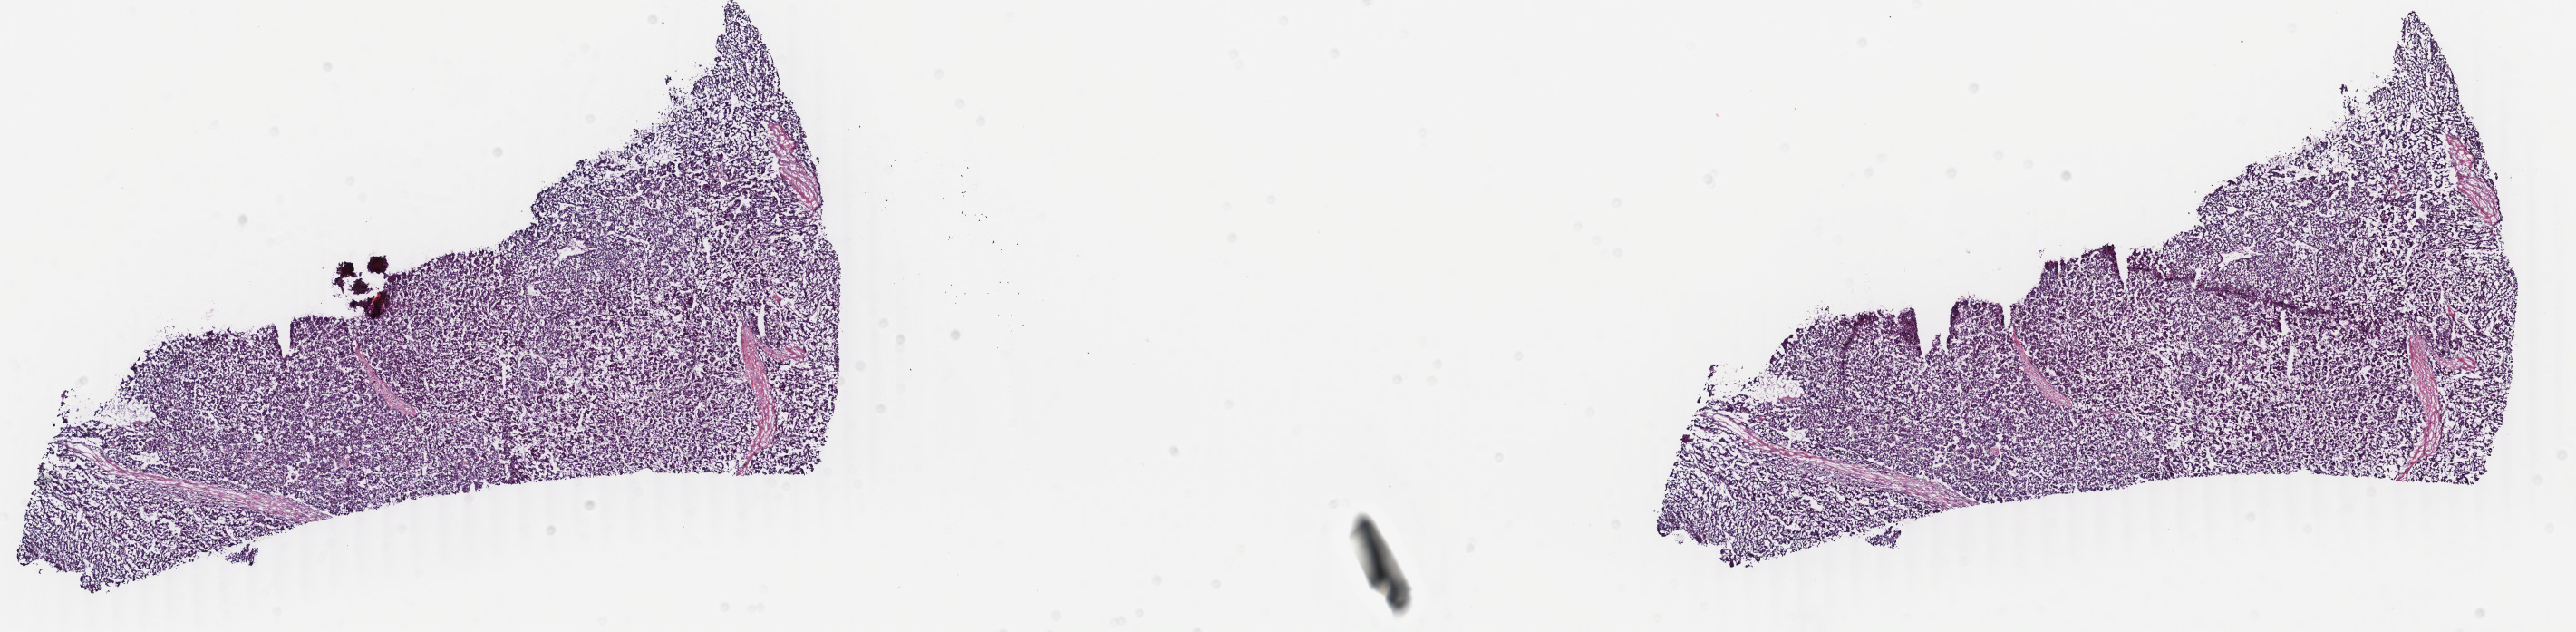
H&E whole-slide image, a low-resolution overview of the entire scanned area, about 22.6 x 5.5 mm (acquisition: 40x scan); frozen section from the top of the tissue portion; primary tumour sample from the liver. Male patient; age at initial diagnosis 50 years. Histologic grade: G3 (poorly differentiated). Slide review estimates, as recorded: tumour cells 90%, tumour nuclei 90%, normal cells 0%, stromal cells 10%, necrosis 0%. Inflammatory infiltration, as recorded: lymphocyte infiltration 2%, monocyte infiltration 0%, neutrophil infiltration 0%.
Pathologic diagnosis: Hepatocellular carcinoma, NOS.